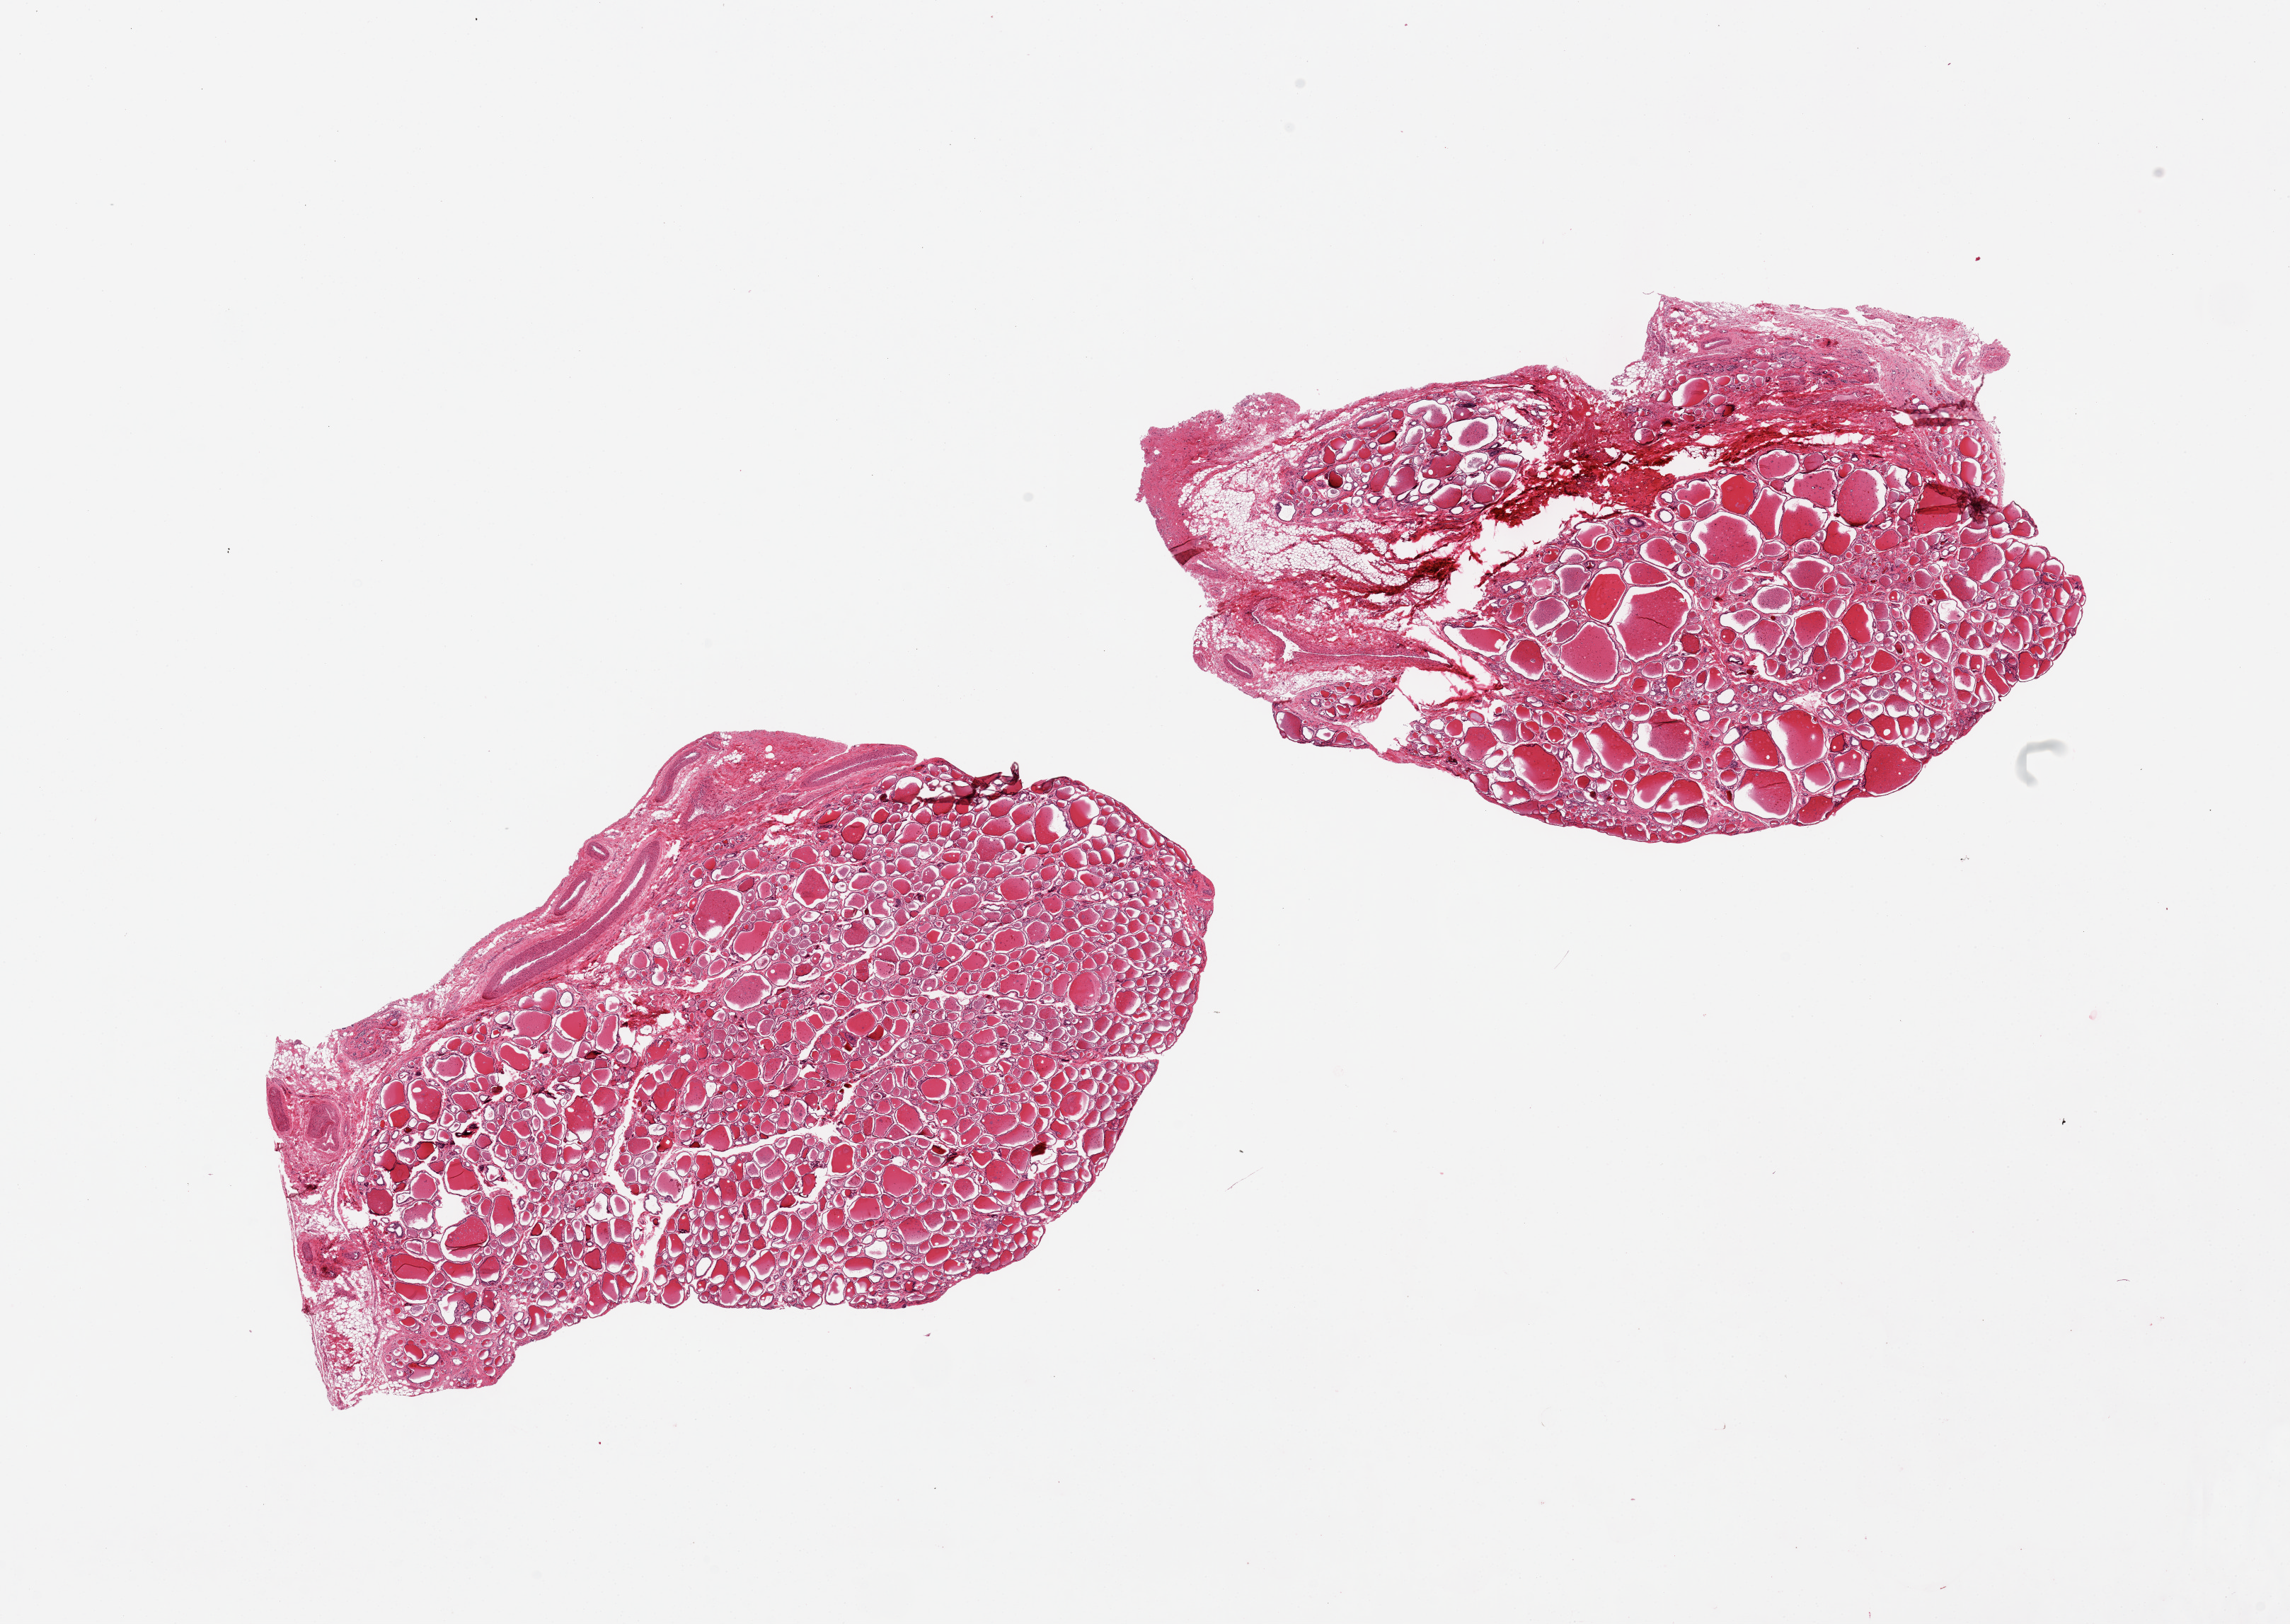
Whole-slide image, haematoxylin and eosin stain — low-resolution overview of the scanned area, about 25.6 x 18.2 mm, PAXgene-fixed, paraffin-embedded tissue, sampled site (target tissue): thyroid, donor tissue sample. Donor sex: male.
Pathologist's review note for this sample: 2 pieces, ~5-10% attached fat and larger vessels, both pieces.